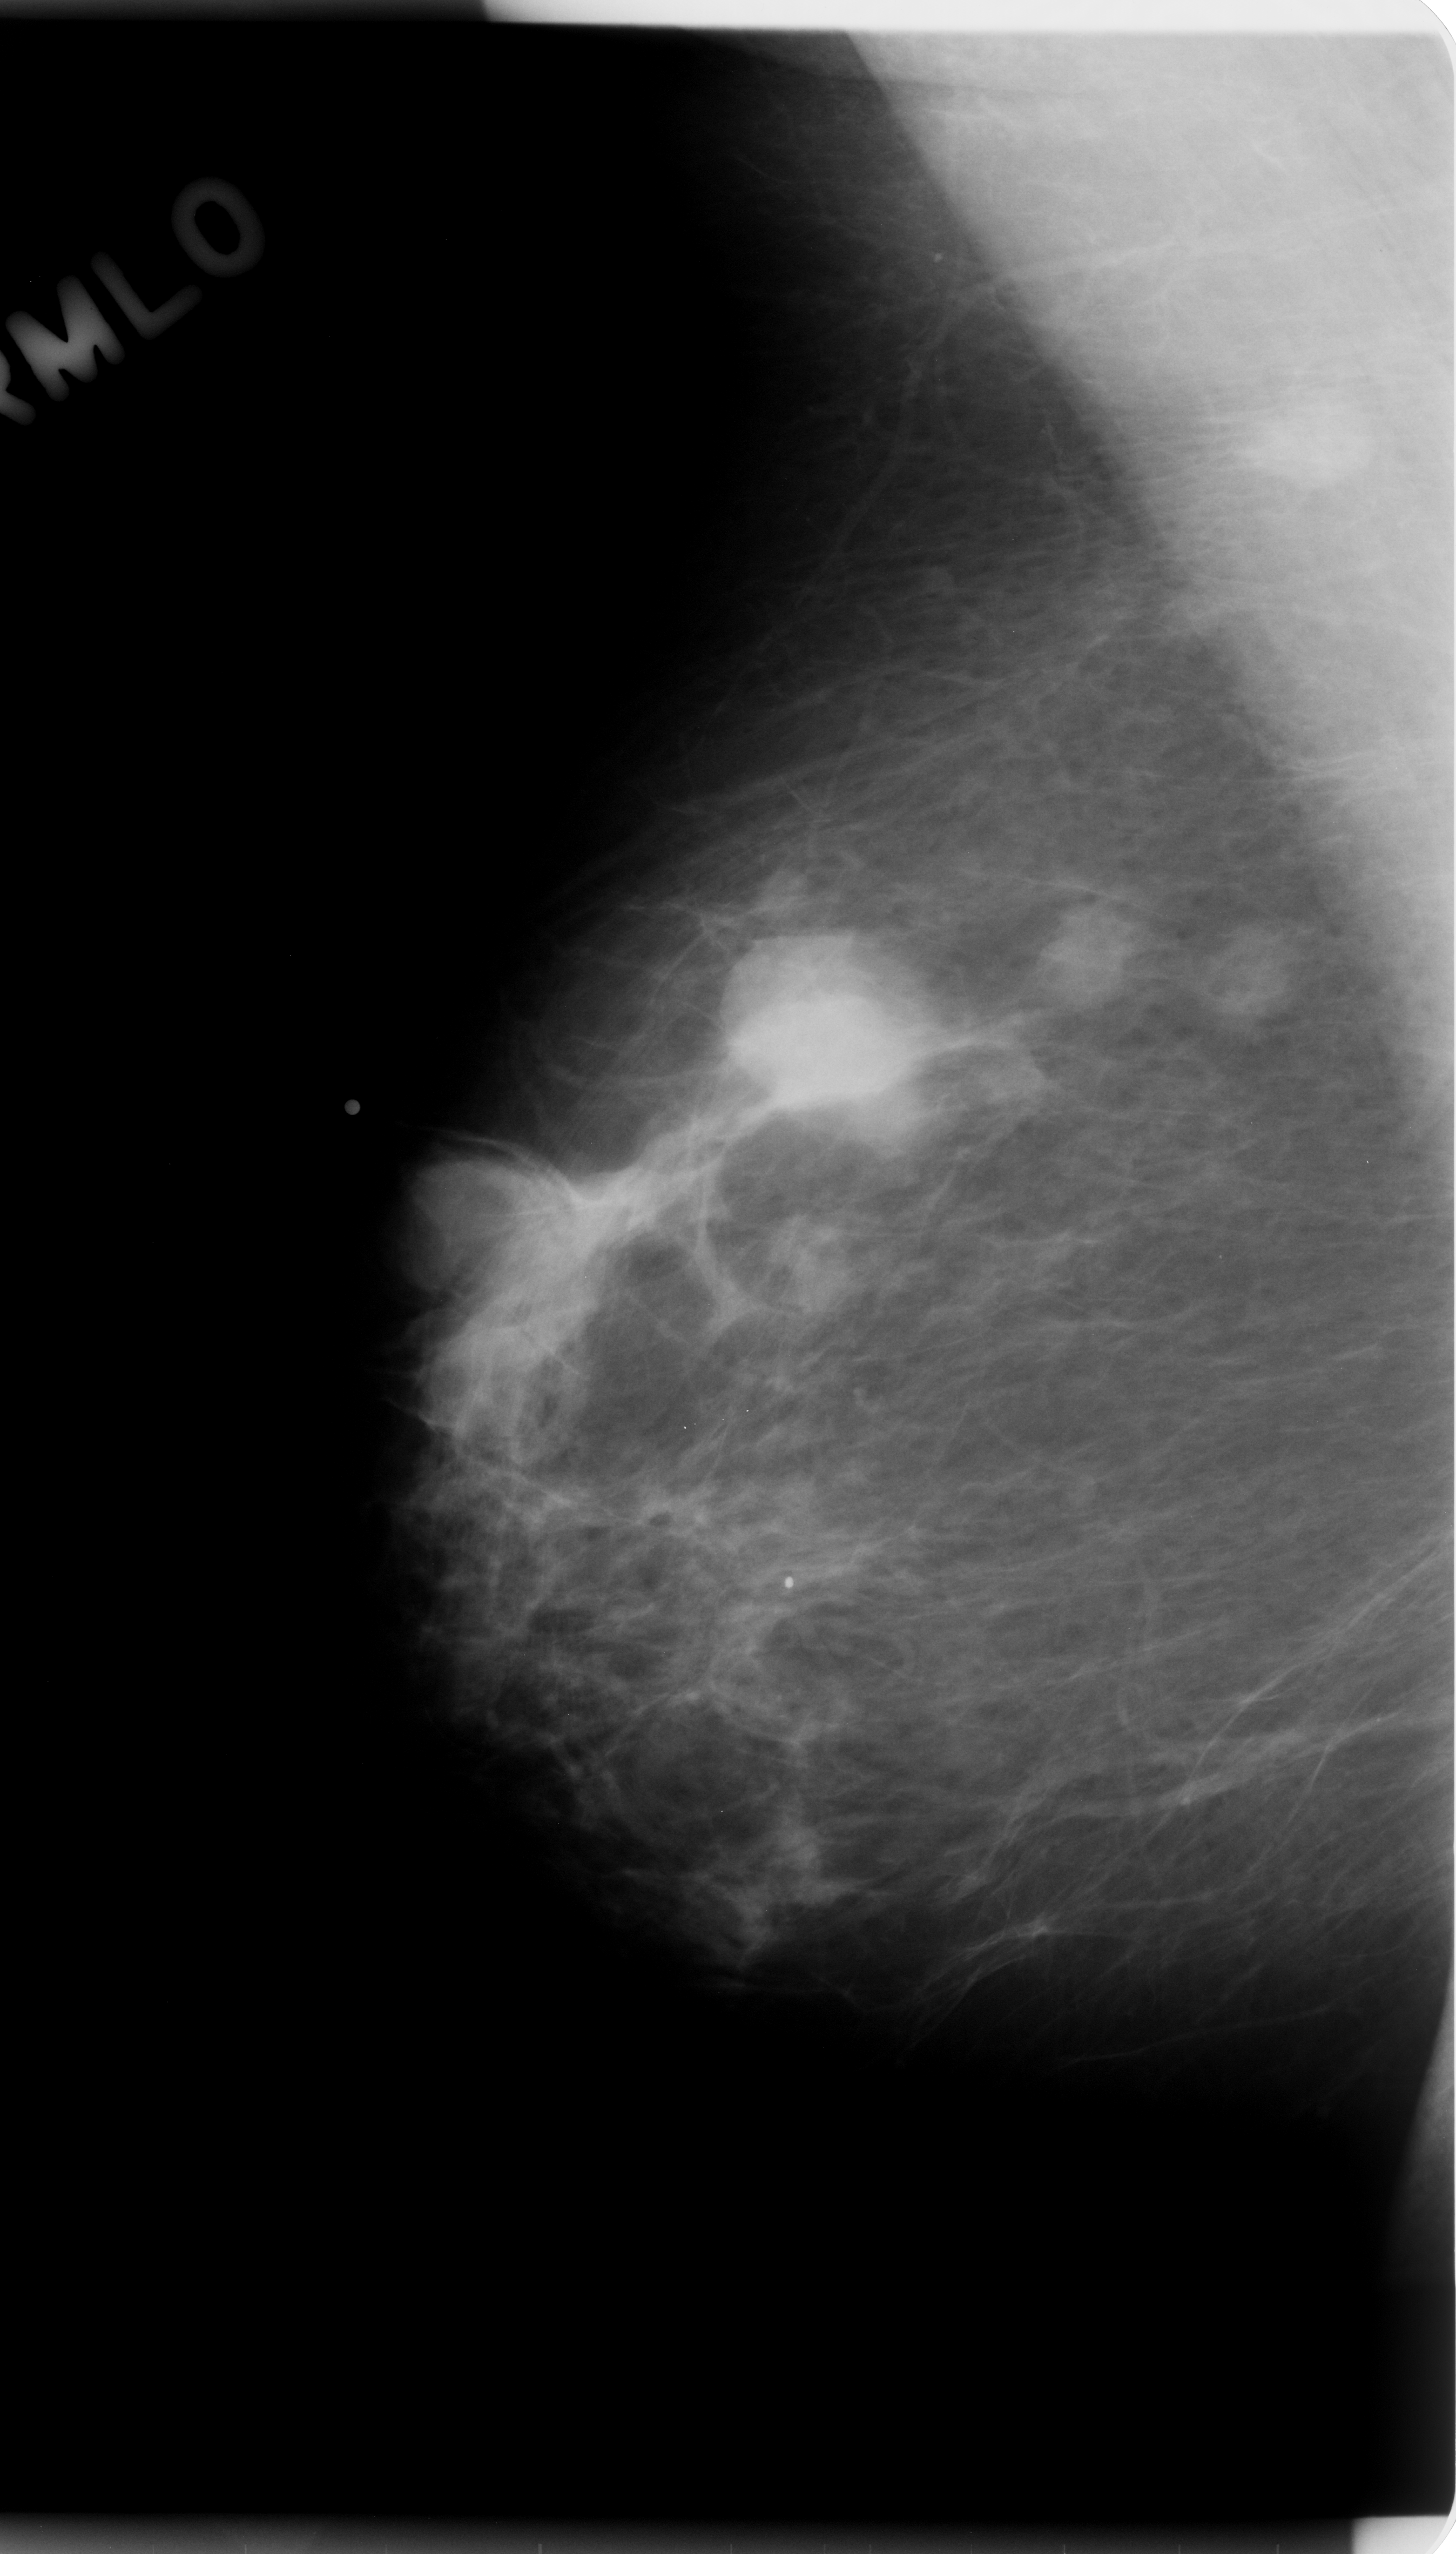
Digitized screen-film mammogram, right breast, MLO view, BI-RADS breast density category 1 (scale 1–4).
Abnormality record for this image: mass, shape lobulated, margins circumscribed; BI-RADS assessment category 5; subtlety rating 5 on a 1 (subtle) to 5 (obvious) scale; pathology (as recorded): malignant.